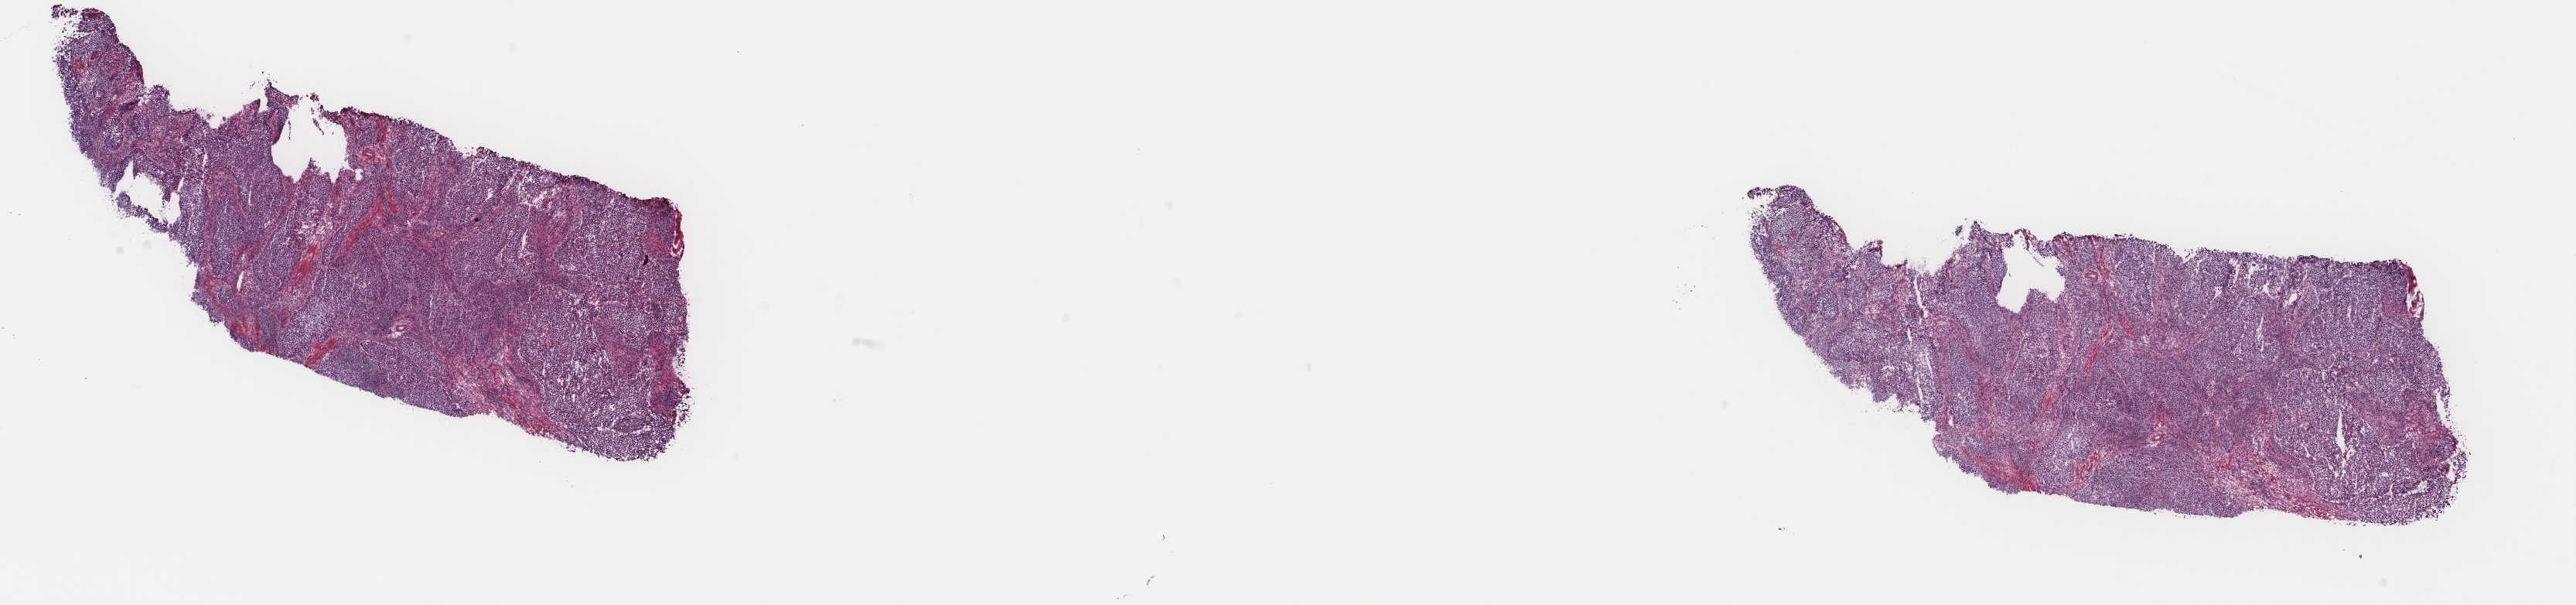
Digitized H&E-stained tissue section (whole slide) — low-resolution overview of the scanned area, about 26.4 x 6.2 mm (from a 40x scan), frozen section from the top of the tissue portion, bladder, primary tumour sample. Patient sex: female. Histologic grade: high grade. Slide review estimates, as recorded: tumour cells 67%, tumour nuclei 75%, normal cells 0%, stromal cells 30%, necrosis 3%. Infiltration values recorded for this section: lymphocyte infiltration 20%, monocyte infiltration 2%, neutrophil infiltration 0%.
AJCC pathologic stage: IV (7th edition). Pathologic diagnosis: Transitional cell carcinoma.